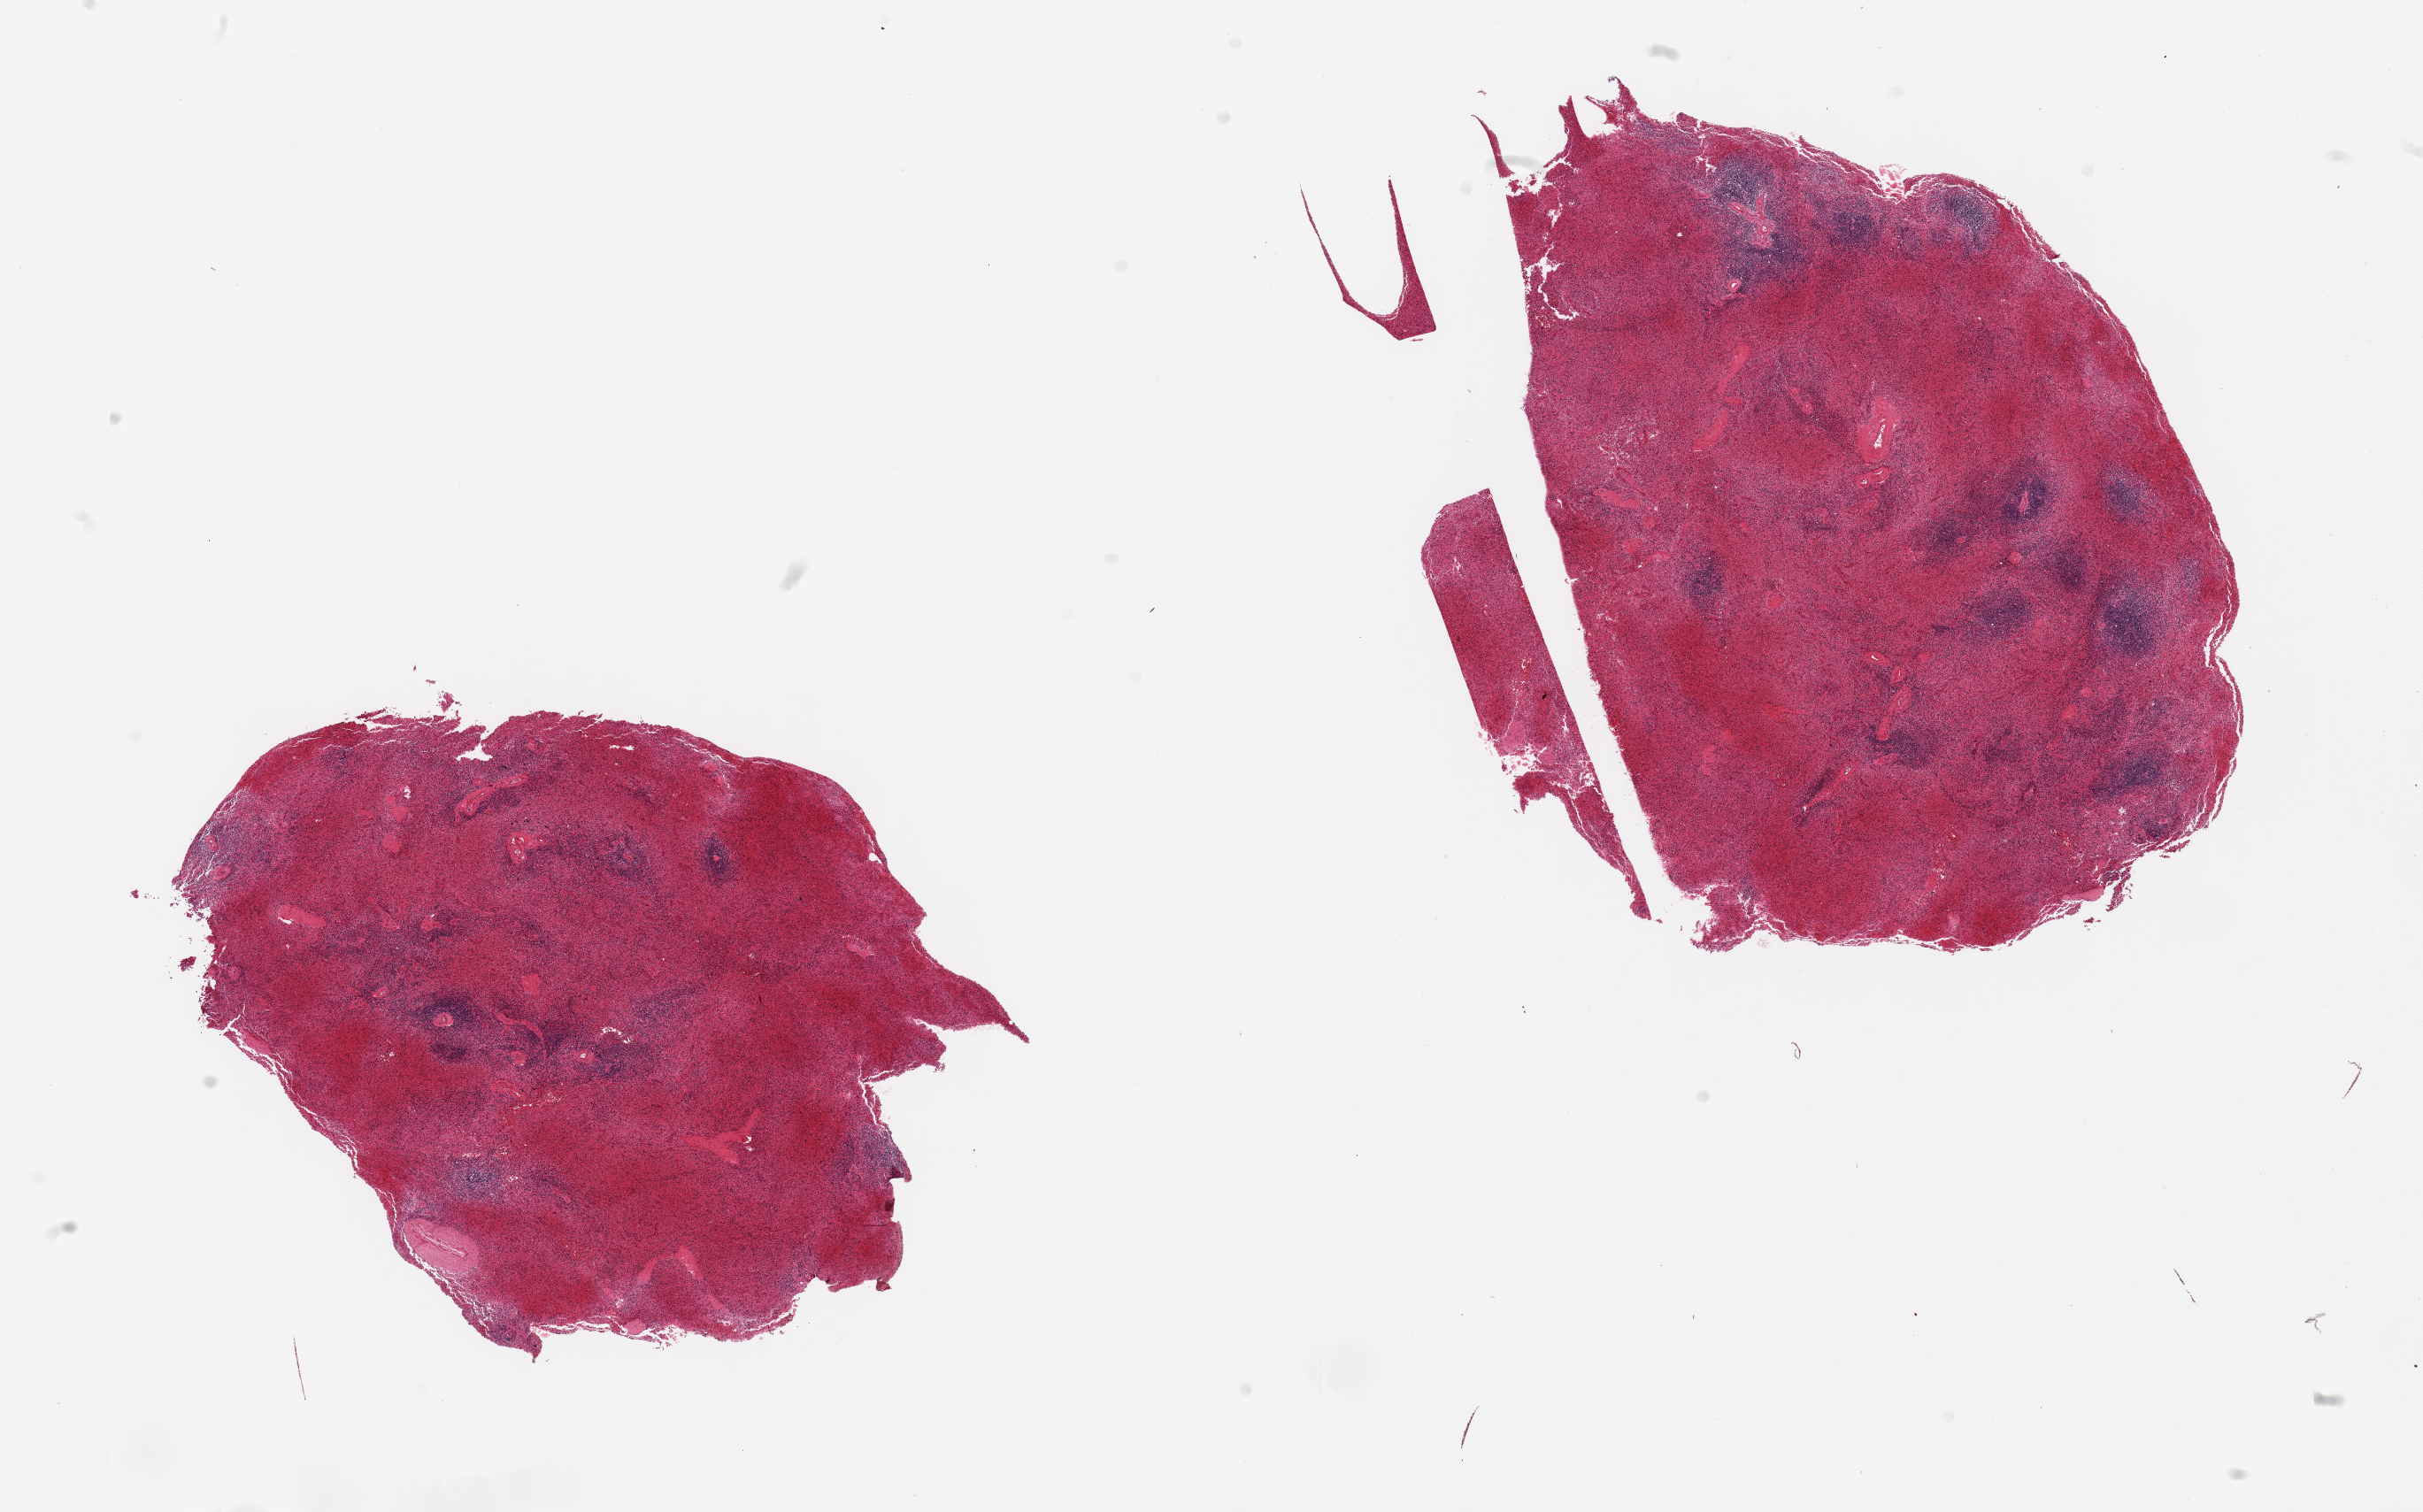
Whole-slide image, hematoxylin and eosin (H&E) stain — a low-resolution overview of the entire scanned area, about 21.7 x 13.5 mm (acquisition: 20x scan). PAXgene-fixed, paraffin-embedded tissue. Section of spleen (target tissue). Tissue donor sample.
Review note (as recorded): 2 pieces ~8x5mm, badly autolyzed.